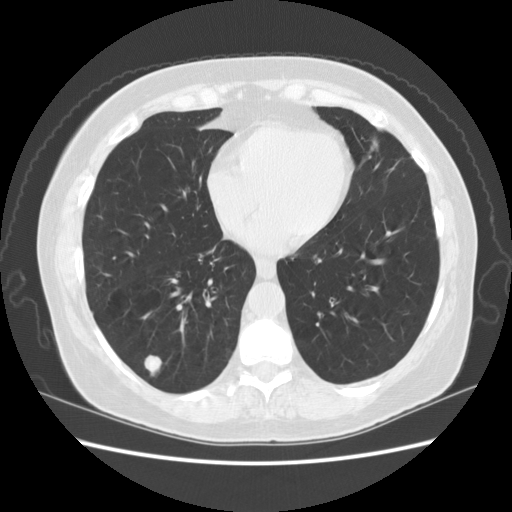
Axial slice from a low-dose chest CT screening exam. Third annual screen. Lung window (W 1500 / L -600 HU). 2.5 mm slice thickness. 120 kVp. Slice 107 of 156 in the series. 512 × 512 image matrix. Female participant, aged 59 years at enrolment. Current smoker at enrolment.
• Expert-annotated lung lesion, bounding box <134,348,172,385> (left, top, right, bottom; pixels).
• The exam's reader record, not a measurement of the box and not confirmed to be the same lesion: non-calcified nodule or mass ≥4 mm, right lower lobe, 16 × 11 mm, smooth margins, soft tissue attenuation, pre-existing on the prior screen: yes; interval growth: yes.
• Lung cancer was diagnosed 42 days after this screen: non-small cell carcinoma, right lower lobe, poorly differentiated (G3), stage IA (AJCC 6th edition), 15 mm at pathology.